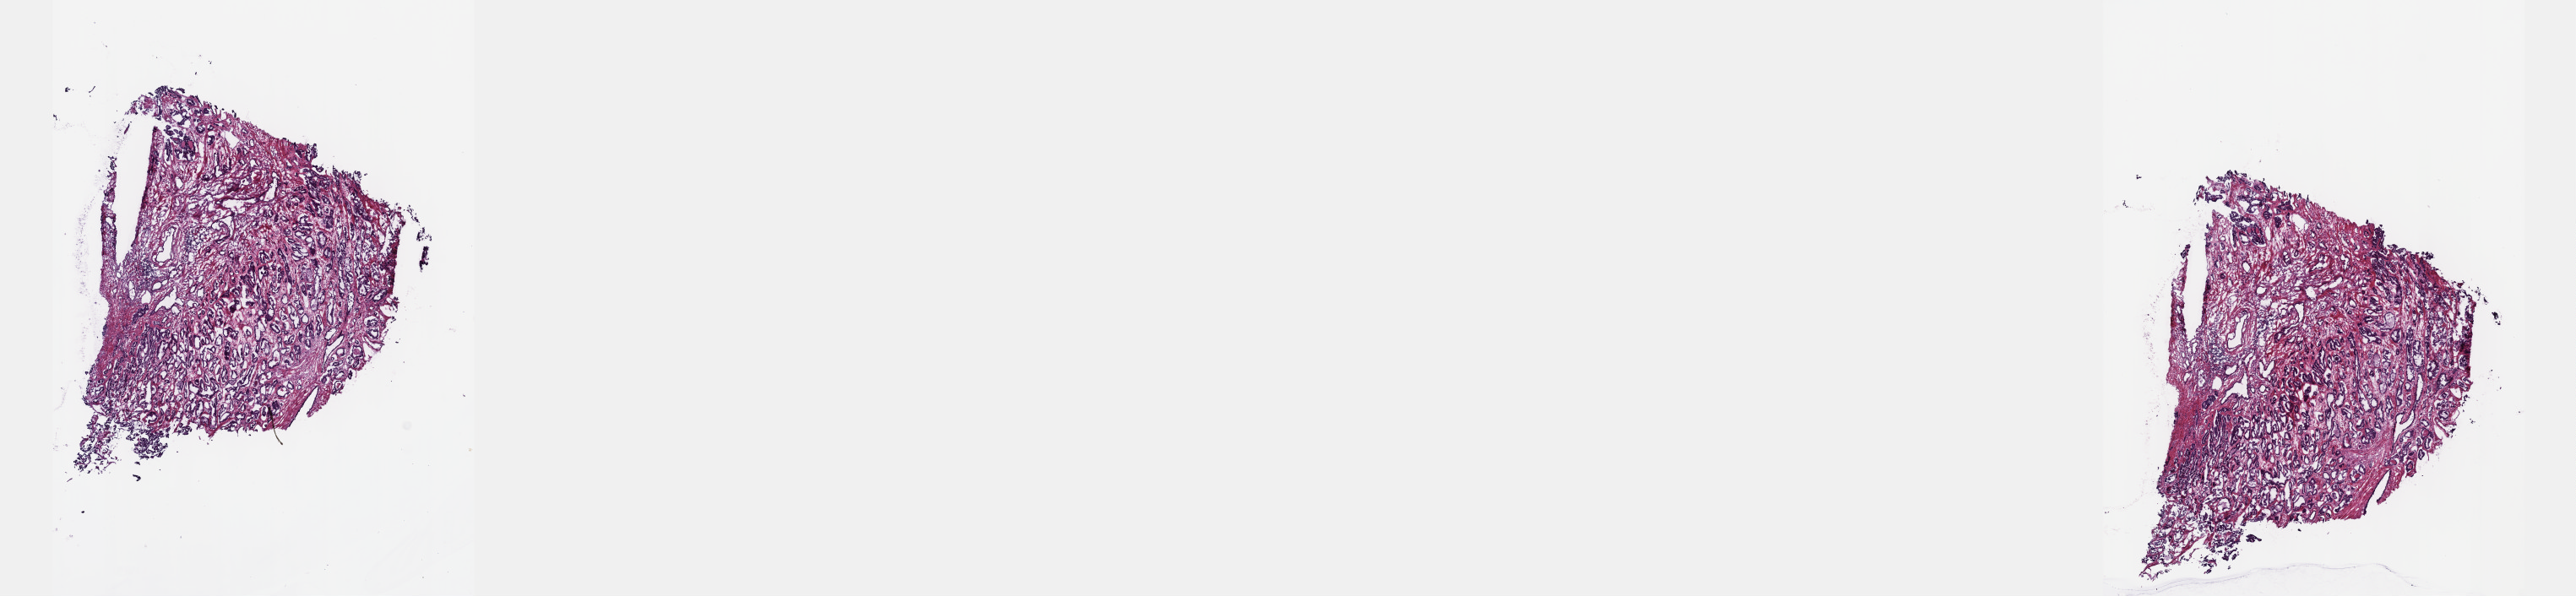
Digitized Hematoxylin and eosin (H&E) stained tissue section (whole slide), low-resolution overview of the scanned area, about 24.6 x 5.7 mm, frozen section, sample: primary tumour, prostate. Male patient; age at initial diagnosis 61 years. Gleason score: 6 (3+3). Pathologist review of this section (percent, as recorded): tumour cells 50%, tumour nuclei 60%, normal cells 20%, stromal cells 30%, necrosis 0%. Inflammatory infiltration, as recorded: lymphocyte infiltration 0%, monocyte infiltration 0%, neutrophil infiltration 0%.
Diagnosis: Adenocarcinoma, NOS (prostate gland).